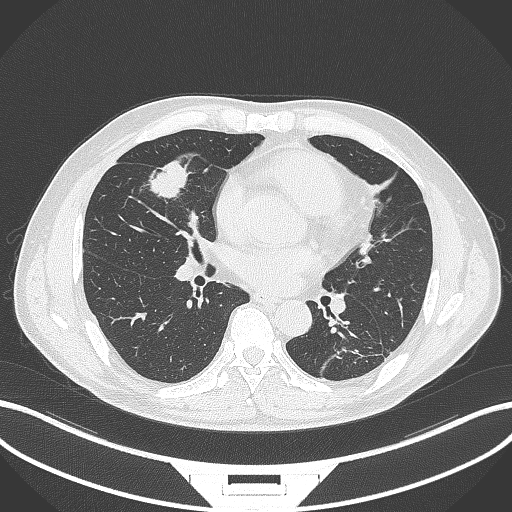
Chest CT, one axial slice. Position 142 of 399 along the scan axis. Reconstruction kernel B70f. 120 kVp. Lung window (W 1500 / L -600 HU). 1 mm slice thickness. 512 × 512 image matrix, field of view 400 × 400 mm. Patient: male, 59 years. From the clinical record (not read from this slice): clinical TNM (as recorded): T2a N1 M0.
Annotated regions visible in this slice (bounding box drawn by a radiologist):
- lung tumour (recorded histology: adenocarcinoma): bounding box (x1, y1, x2, y2) in pixels: (145, 158, 190, 203)